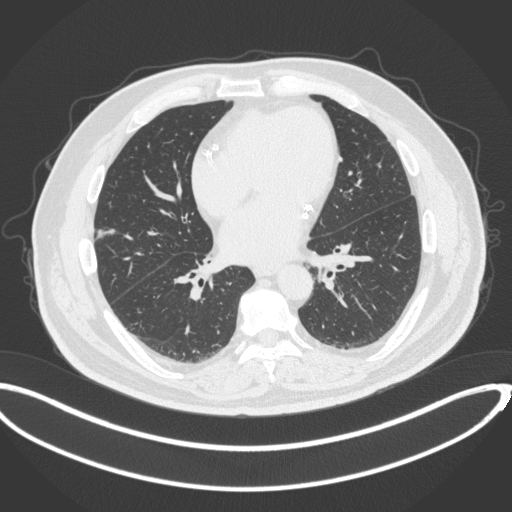
Chest CT, one axial slice. Slice 143 of 342 in the series (ordered by position). Reconstruction kernel B31f. 120 kVp. Lung window (W 1500 / L -600 HU). 1 mm slice thickness. 512 × 512 image matrix. Patient: male, 68 years. Case-level facts recorded for this patient, not image findings: clinical TNM (as recorded): T1c N0 M0; histopathological grade: G2.
Structures marked on this image (bounding box drawn by a radiologist):
- lung tumour (recorded histology: adenocarcinoma): box from (x=95, y=229) to (x=117, y=239) px